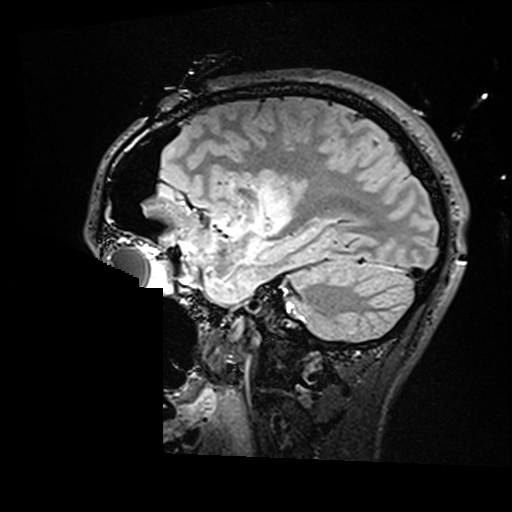
Brain MRI from a brain-tumour surgery series, one sagittal slice. Position 114 of 176 along the scan axis. T2 FLAIR. 1 mm slice thickness. 512 × 512 image matrix, field of view 250 × 250 mm. Case-level facts recorded for this patient, not image findings: histopathology: Astrocytoma; WHO grade: 2; IDH mutation: yes.
Annotated regions visible in this slice (outlined manually by an expert reader):
- residual tumour: bounding box <260,184,288,230> (left, top, right, bottom; pixels)